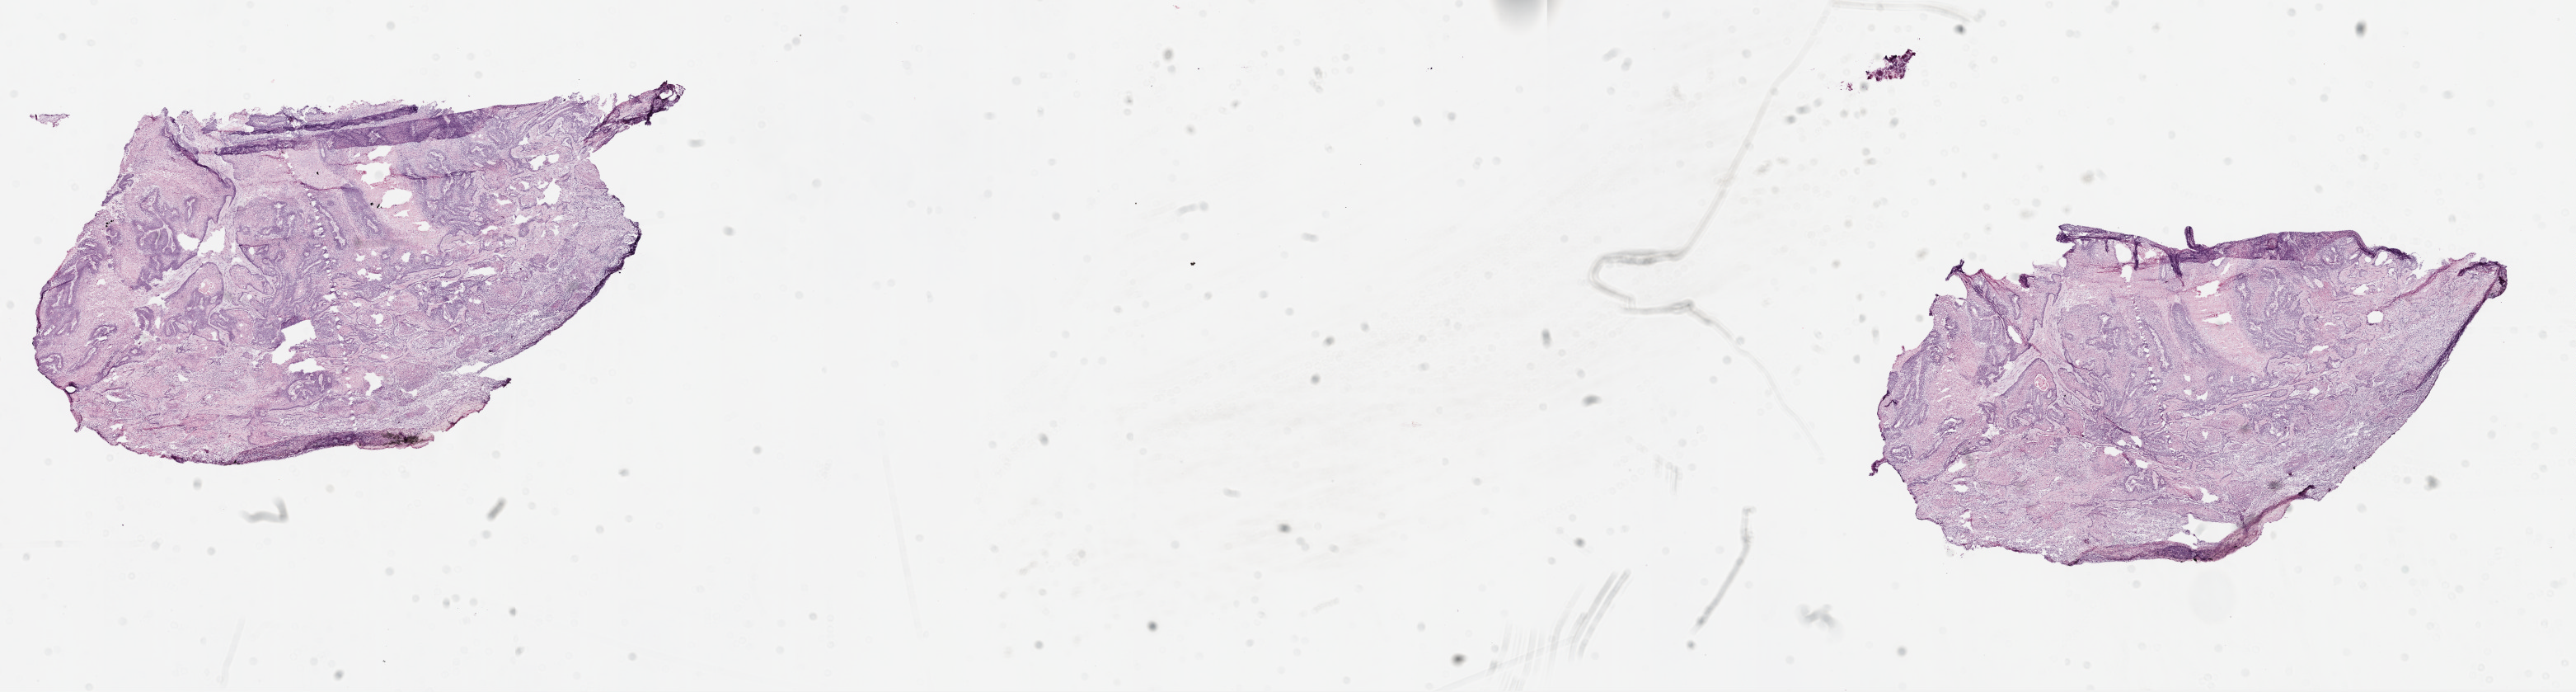
Digitized H&E tissue section (whole slide), a low-resolution overview of the entire scanned area, about 25.1 x 6.7 mm (slide scanned at 20x), frozen section from the top of the tissue portion, primary tumour sample from the lung. Patient: male, age at initial diagnosis 39 years. Composition of this section per pathologist review: tumour cells 78%, tumour nuclei 80%, normal cells 0%, stromal cells 15%, necrosis 7%.
AJCC pathologic stage: IIB. Laterality: left. Diagnosis: Squamous cell carcinoma, NOS. TNM: T2 N1 M0.